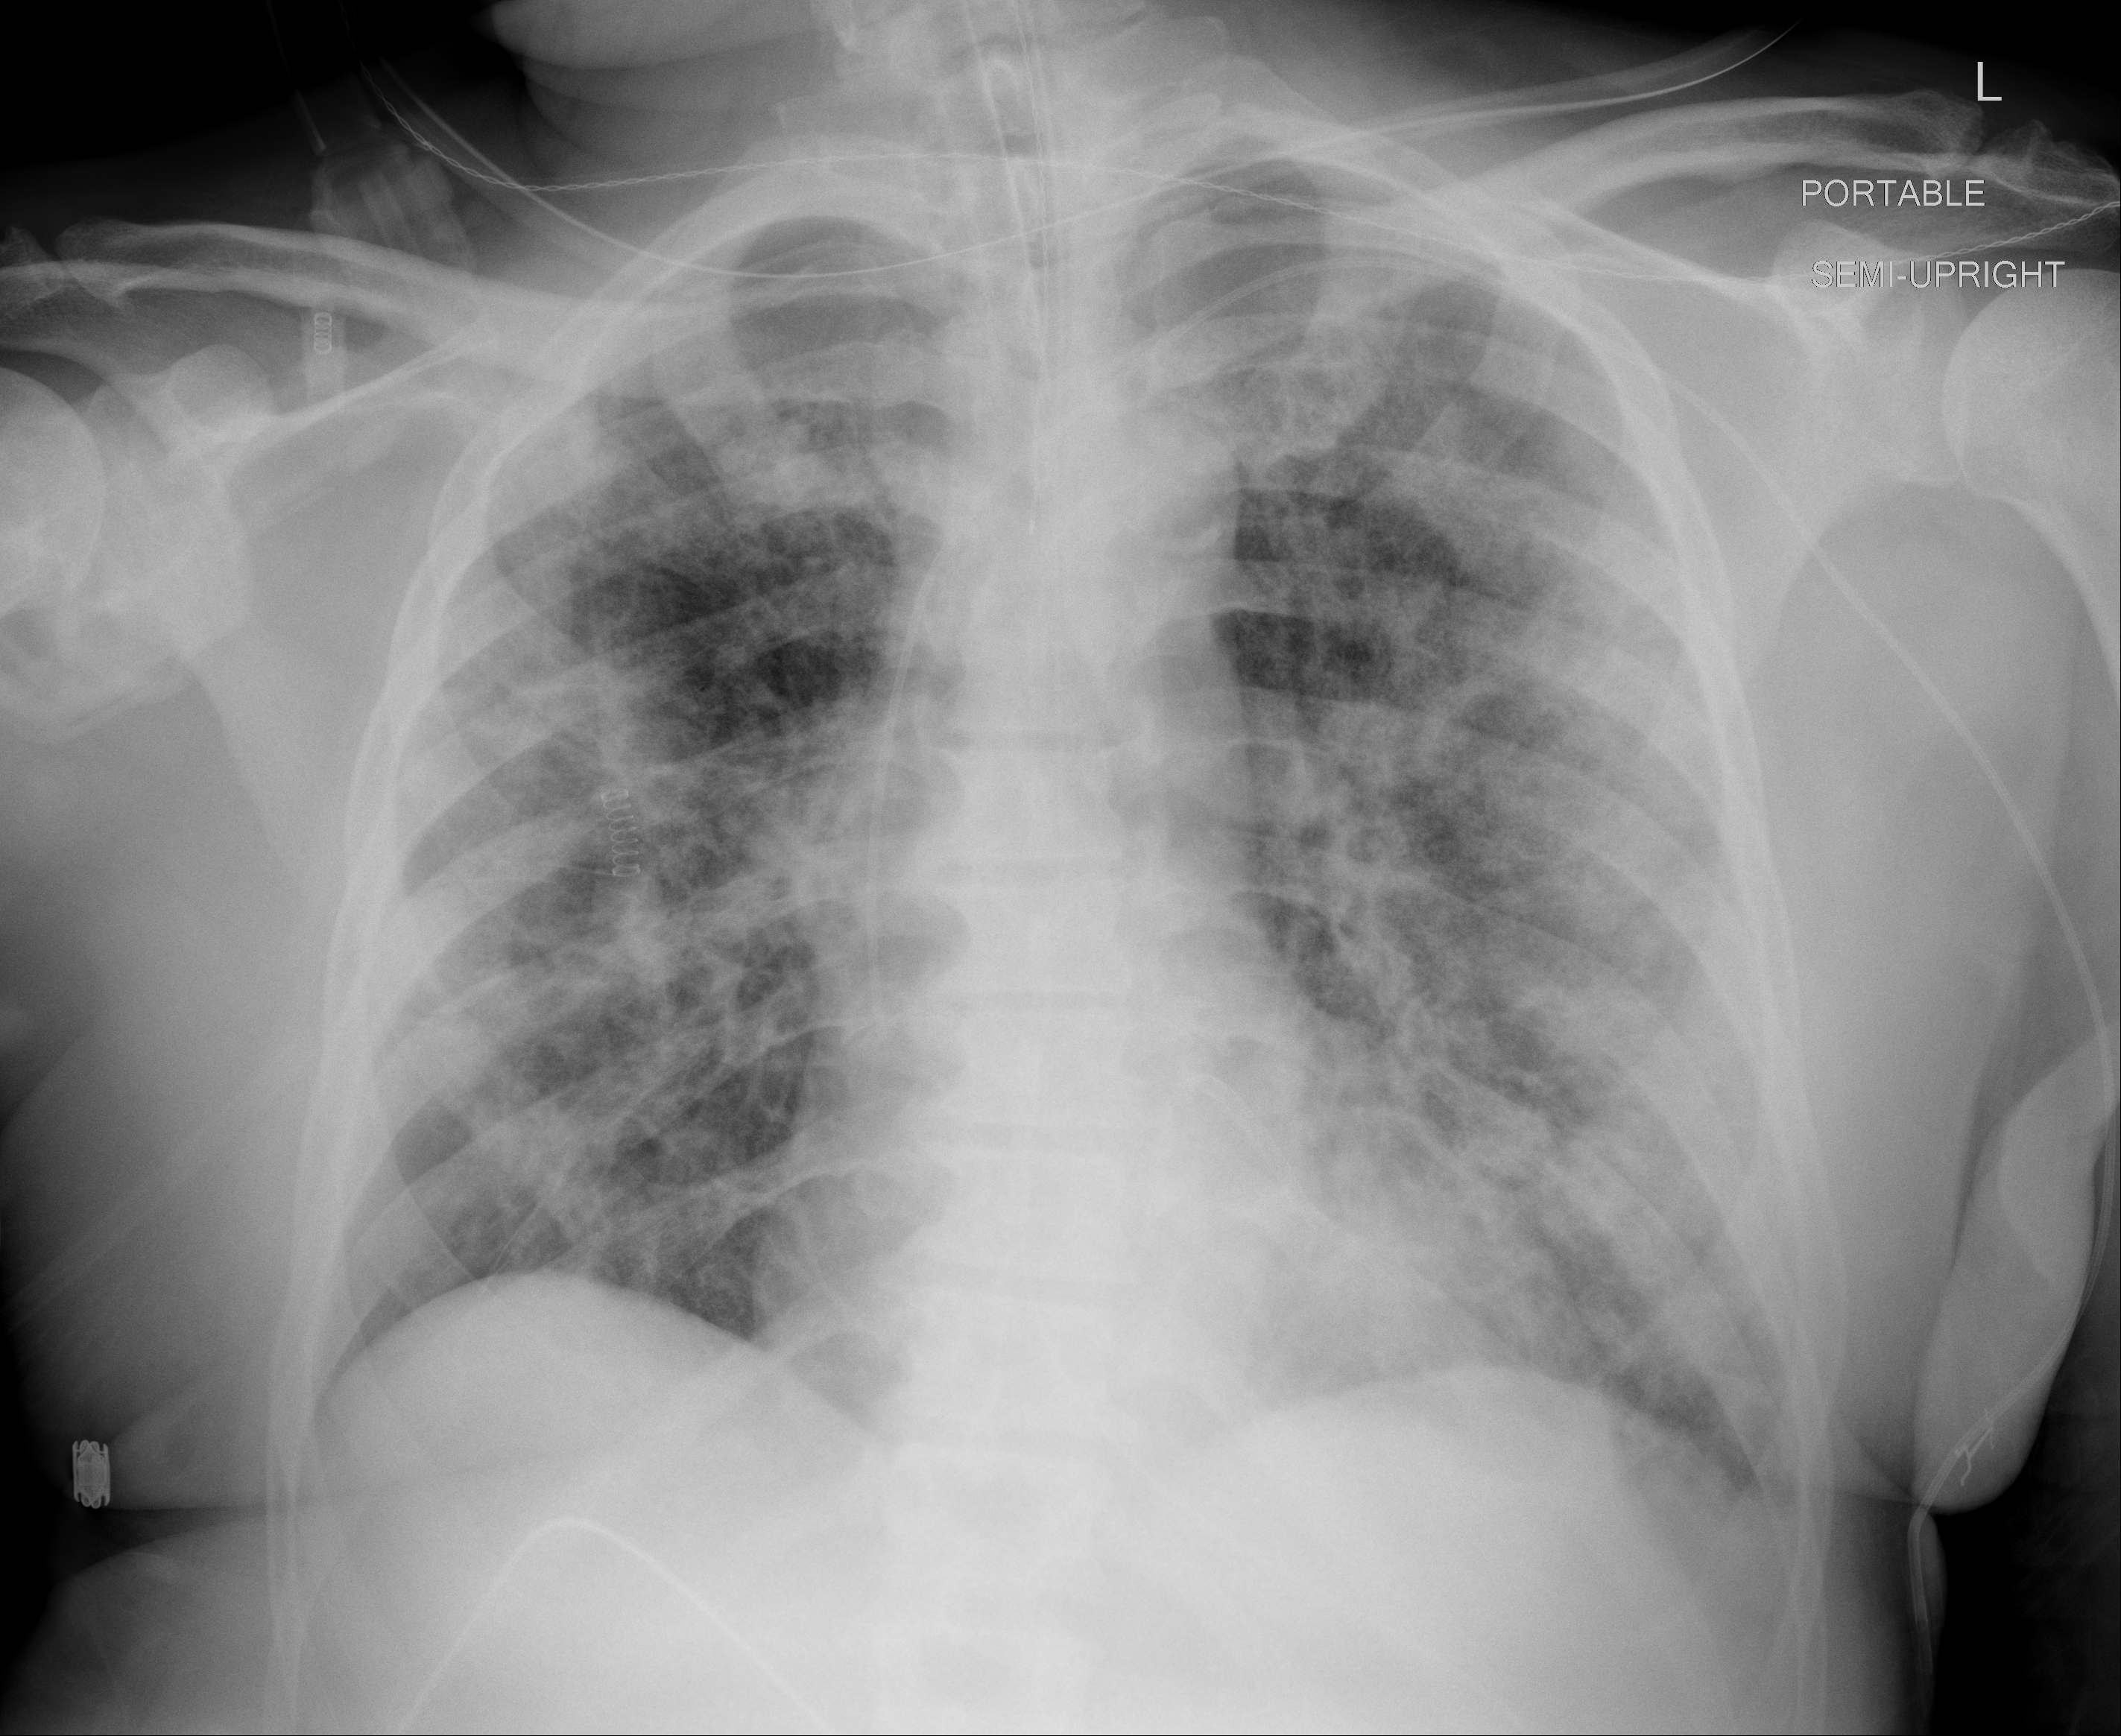
Portable chest radiograph, AP projection. Male patient, age 64 years; imaged 6 days after the COVID-19 diagnosis.
Radiologist's key findings for this exam: Patchy airspace opacities throughout both lungs, without significant change.